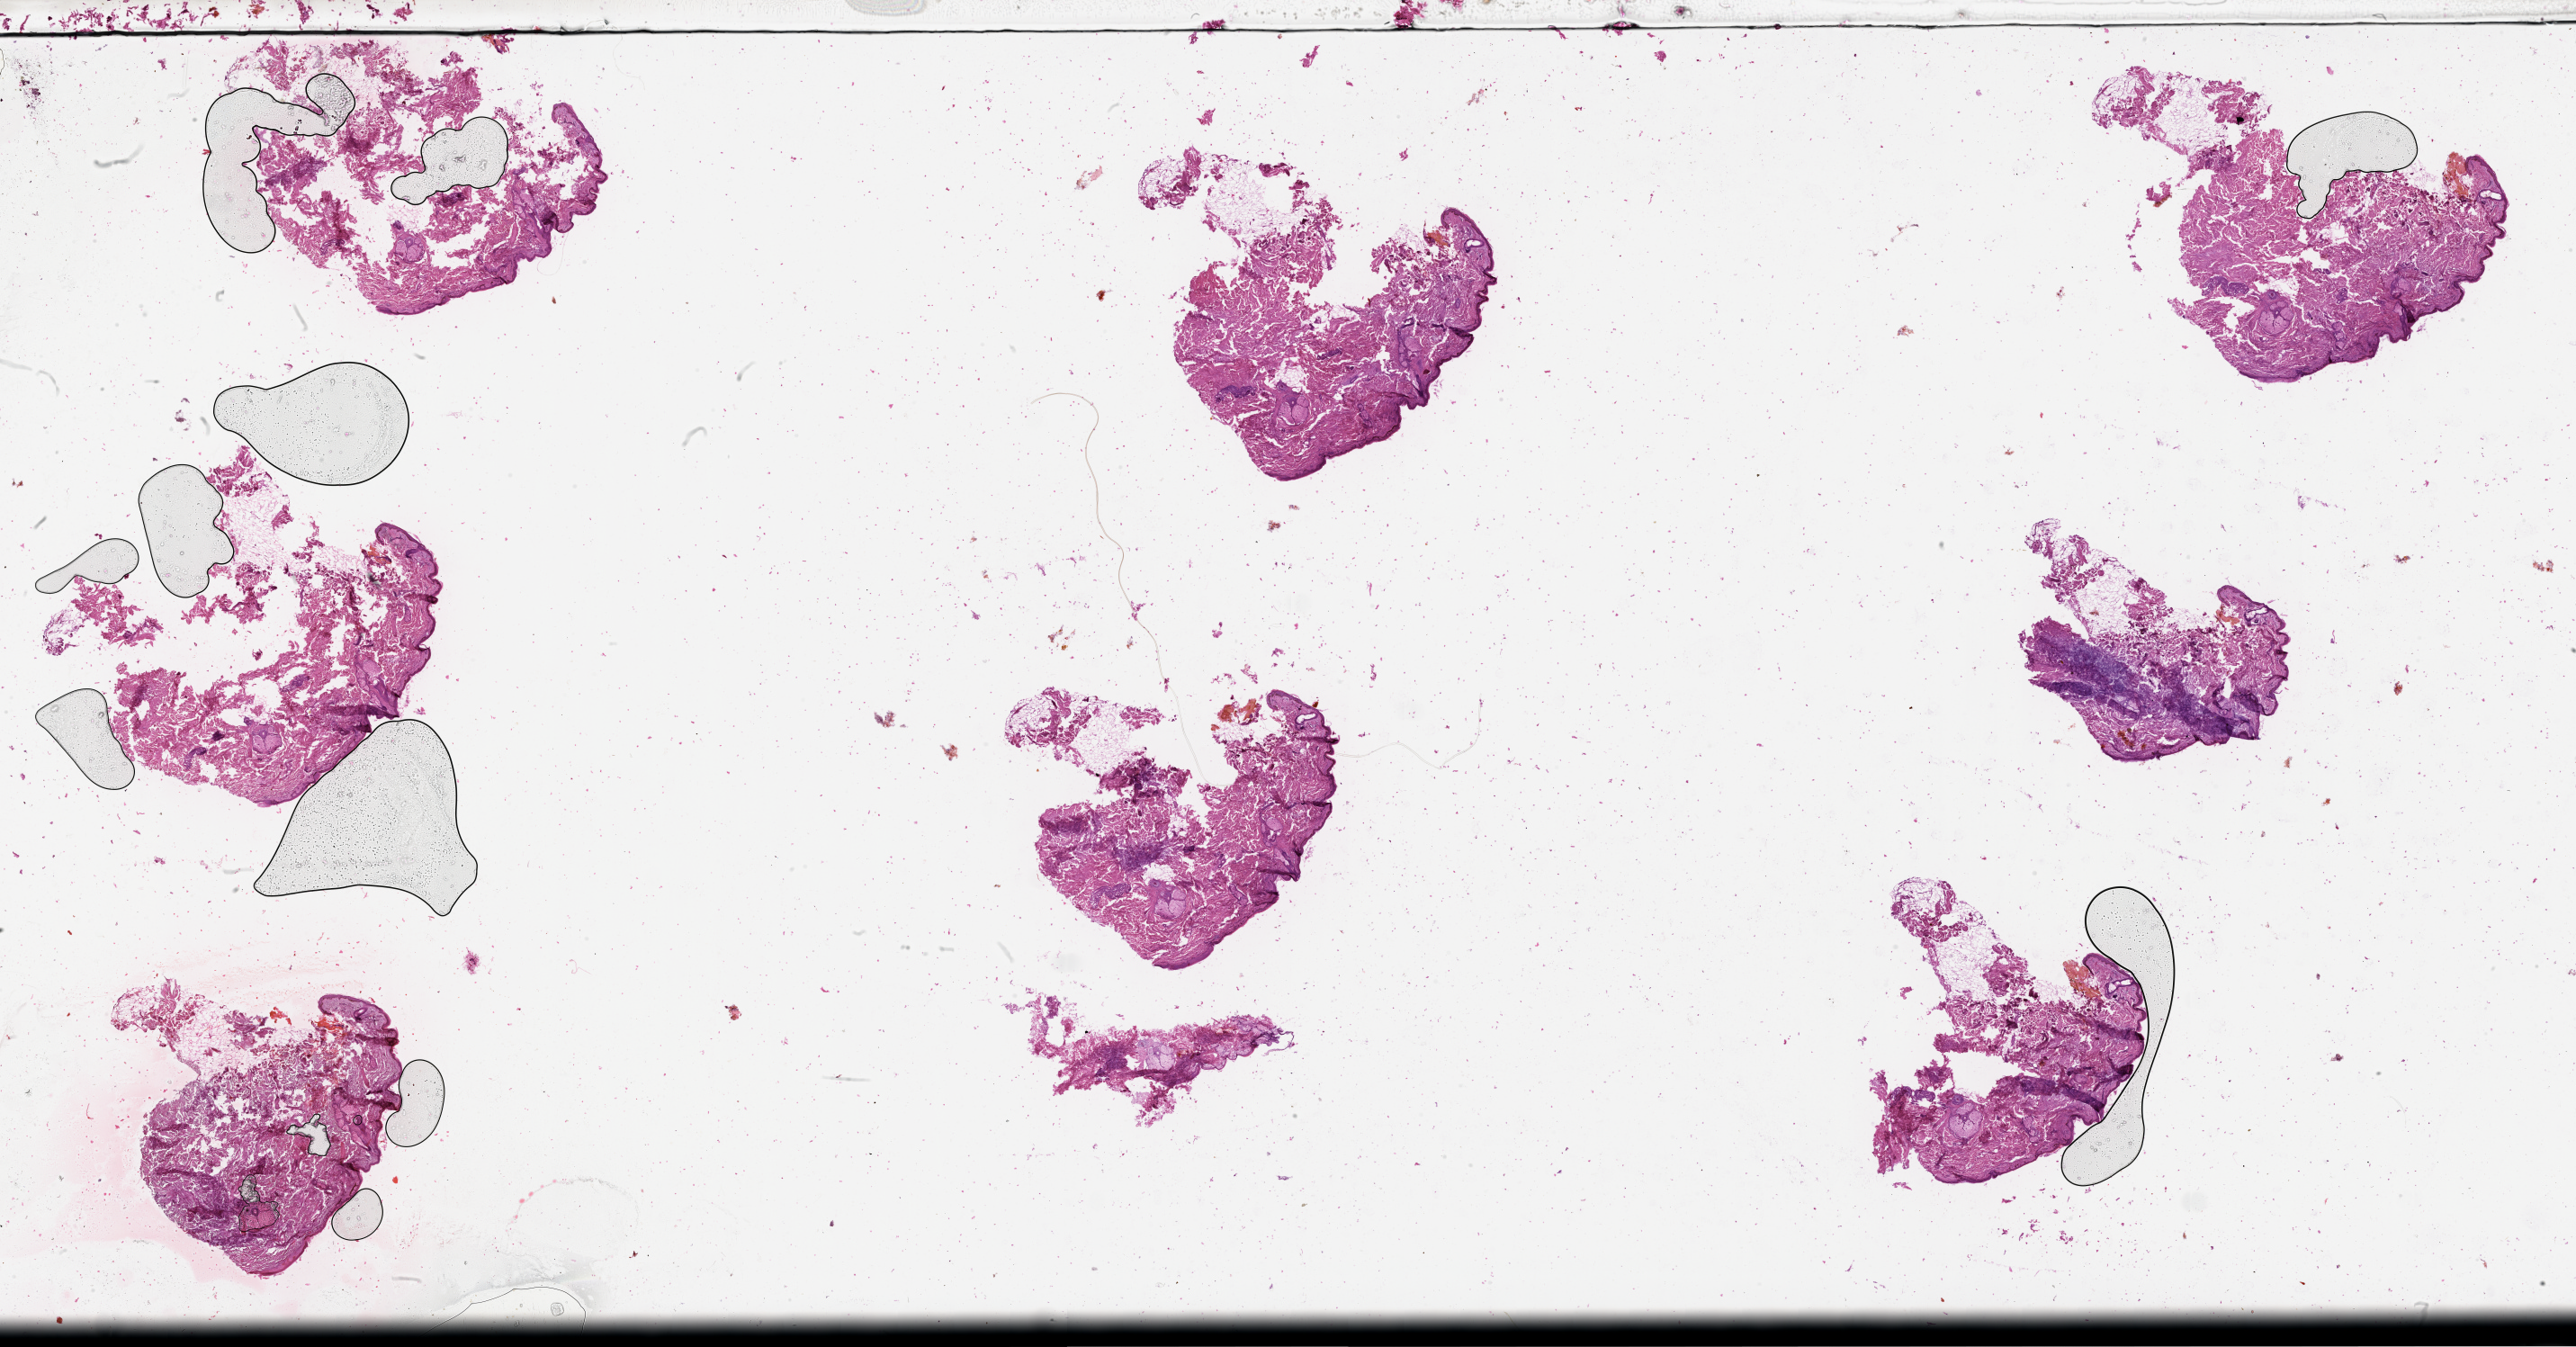
Whole-slide histology image, H&E, whole scanned area (about 46.1 x 24.1 mm, slide scanned at 20x) shown as a low-resolution overview.
* patient diagnosis (cohort enrolment): cutaneous melanoma (skin)